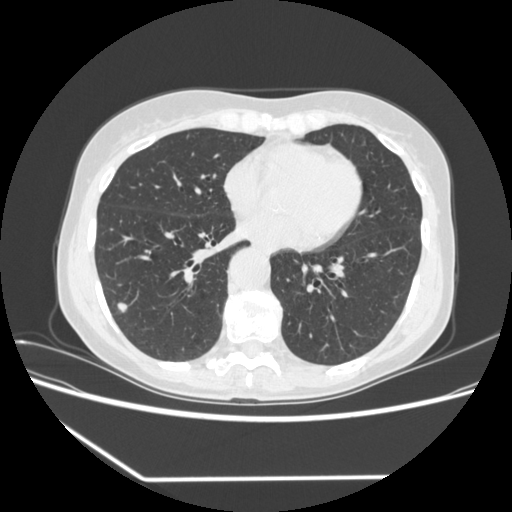
Low-dose screening chest CT, one axial slice. Position 155 of 323 along the scan axis. Reconstruction kernel STANDARD. 120 kVp. Lung window (W 1500 / L -600 HU). 1.25 mm slice thickness. 512 × 512 image matrix.
Structures marked on this image (expert manual segmentation):
- lesion 2 (nodule, lower lobe of right lung): box from (x=117, y=302) to (x=128, y=313) px